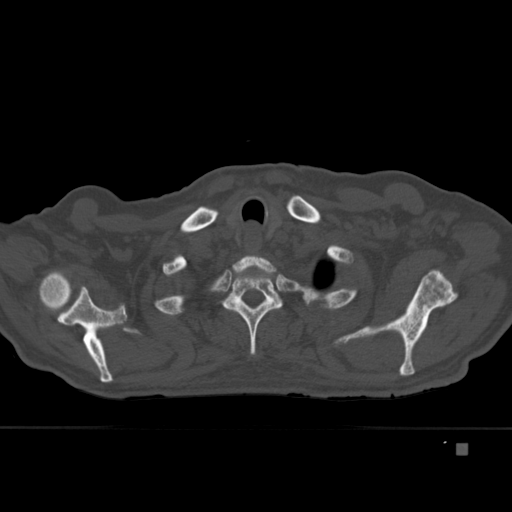
CT including the spine, one axial slice; slice 348 of 451 in the series (ordered by position); bone window (W 1800 / L 400 HU); 1.5 mm slice thickness; 512 × 512 image matrix, field of view 378 × 378 mm. Male patient, age 75 years. Case-level facts recorded for this patient, not image findings: primary cancer: prostate.
Structures marked on this image (semi-automatically segmented with operator editing):
- T1 vertebra: box from (x=232, y=255) to (x=277, y=284) px
- T2 vertebra: (x=217, y=258)–(x=283, y=355)